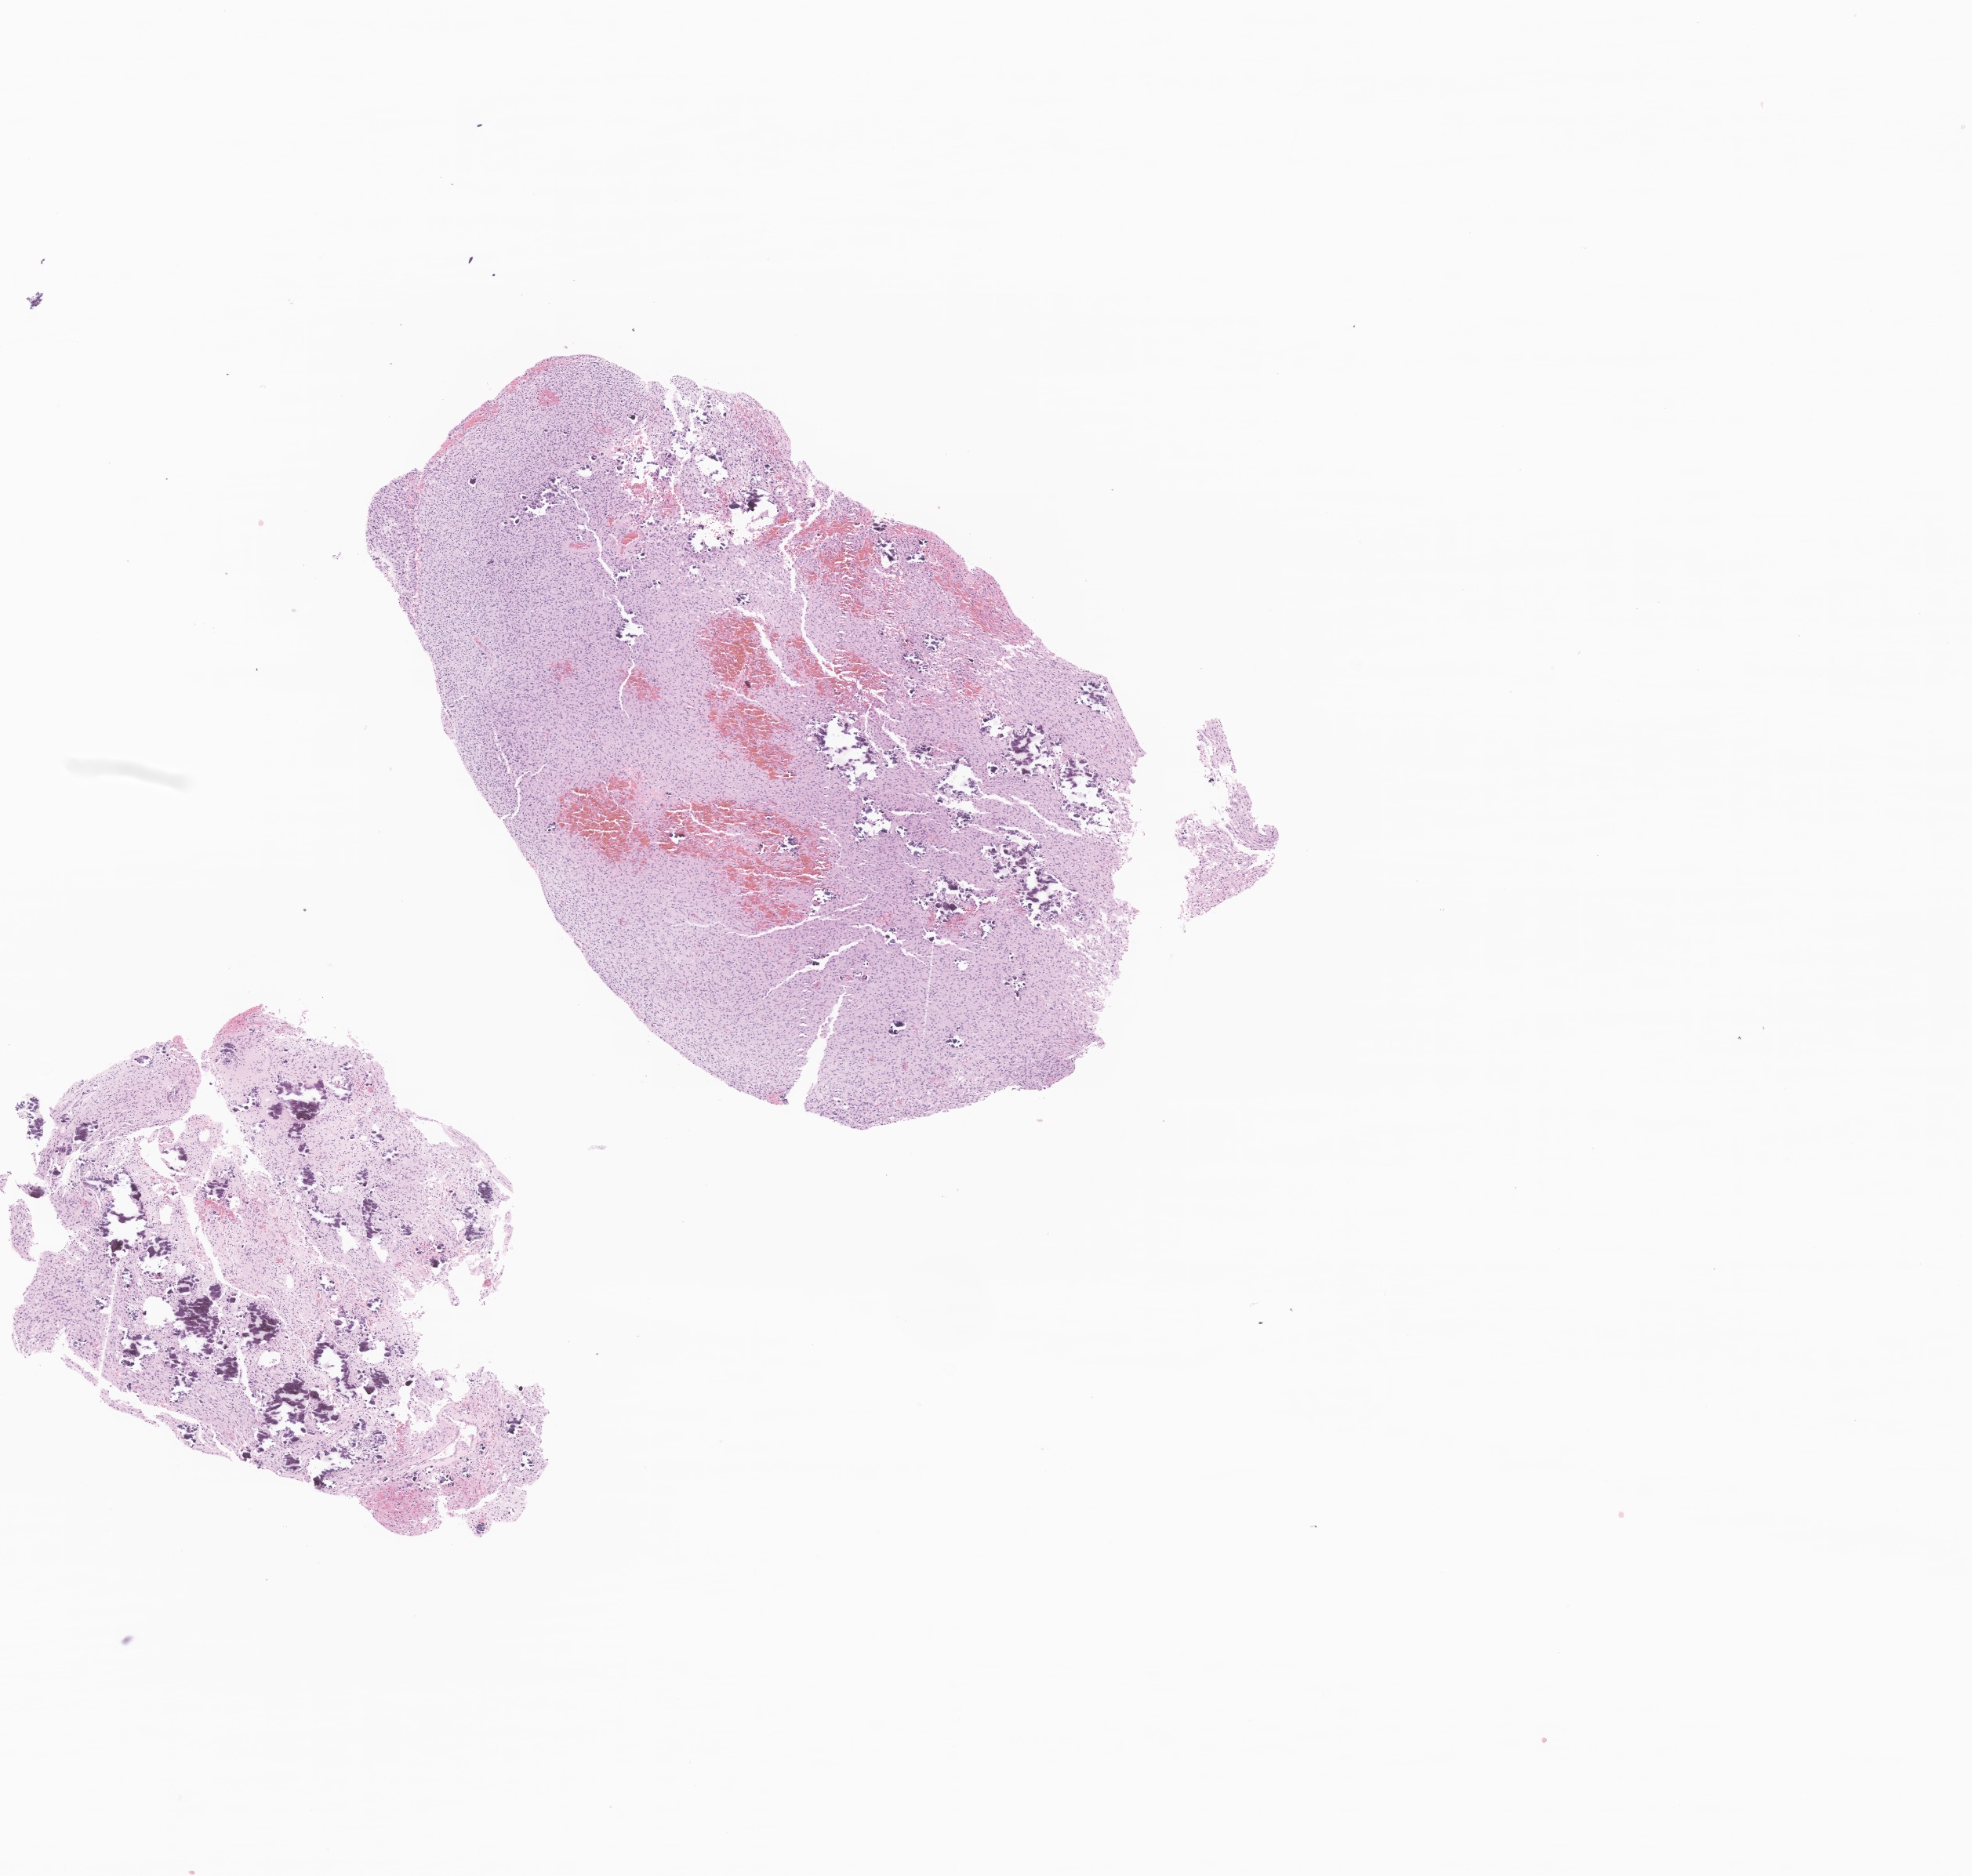
Whole-slide image, haematoxylin and eosin stain of tumor tissue from the temporal lobe, low-resolution overview of the scanned area, about 10.6 x 10.1 mm, formalin-fixed paraffin-embedded section. Patient male; age 71 months (5 years 11 months).
Diagnosis (ICD-O-3 morphology term): Dysembryoplastic neuroepithelial tumor.